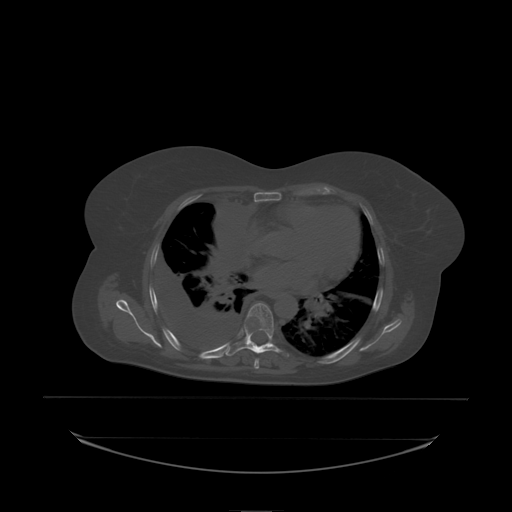
CT including the spine, one axial slice. Slice 143 of 242 in the series (ordered by position). Bone window (W 1800 / L 400 HU). 2.5 mm slice thickness. 512 × 512 image matrix. Female patient, age 53 years. Case-level facts recorded for this patient, not image findings: primary cancer: lung.
Structures marked on this image (semi-automatic segmentation, software-assisted and operator-edited):
- T7 vertebra: bounding box <245,303,274,338> (left, top, right, bottom; pixels)